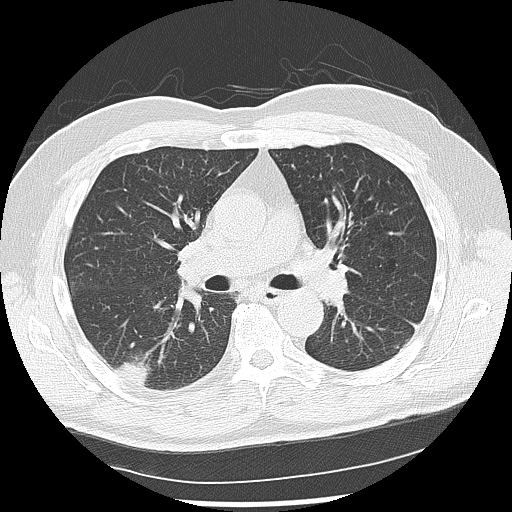
Low-dose screening chest CT, one axial slice. Slice 78 of 142 in the series (ordered by position). Reconstruction kernel LUNG. 120 kVp. Lung window (W 1500 / L -600 HU). 512 × 512 image matrix, field of view 360 × 360 mm.
Outlined on this slice (expert manual segmentation):
- lesion 2 (nodule, lower lobe of right lung): bounding box <117,359,151,385> (left, top, right, bottom; pixels)